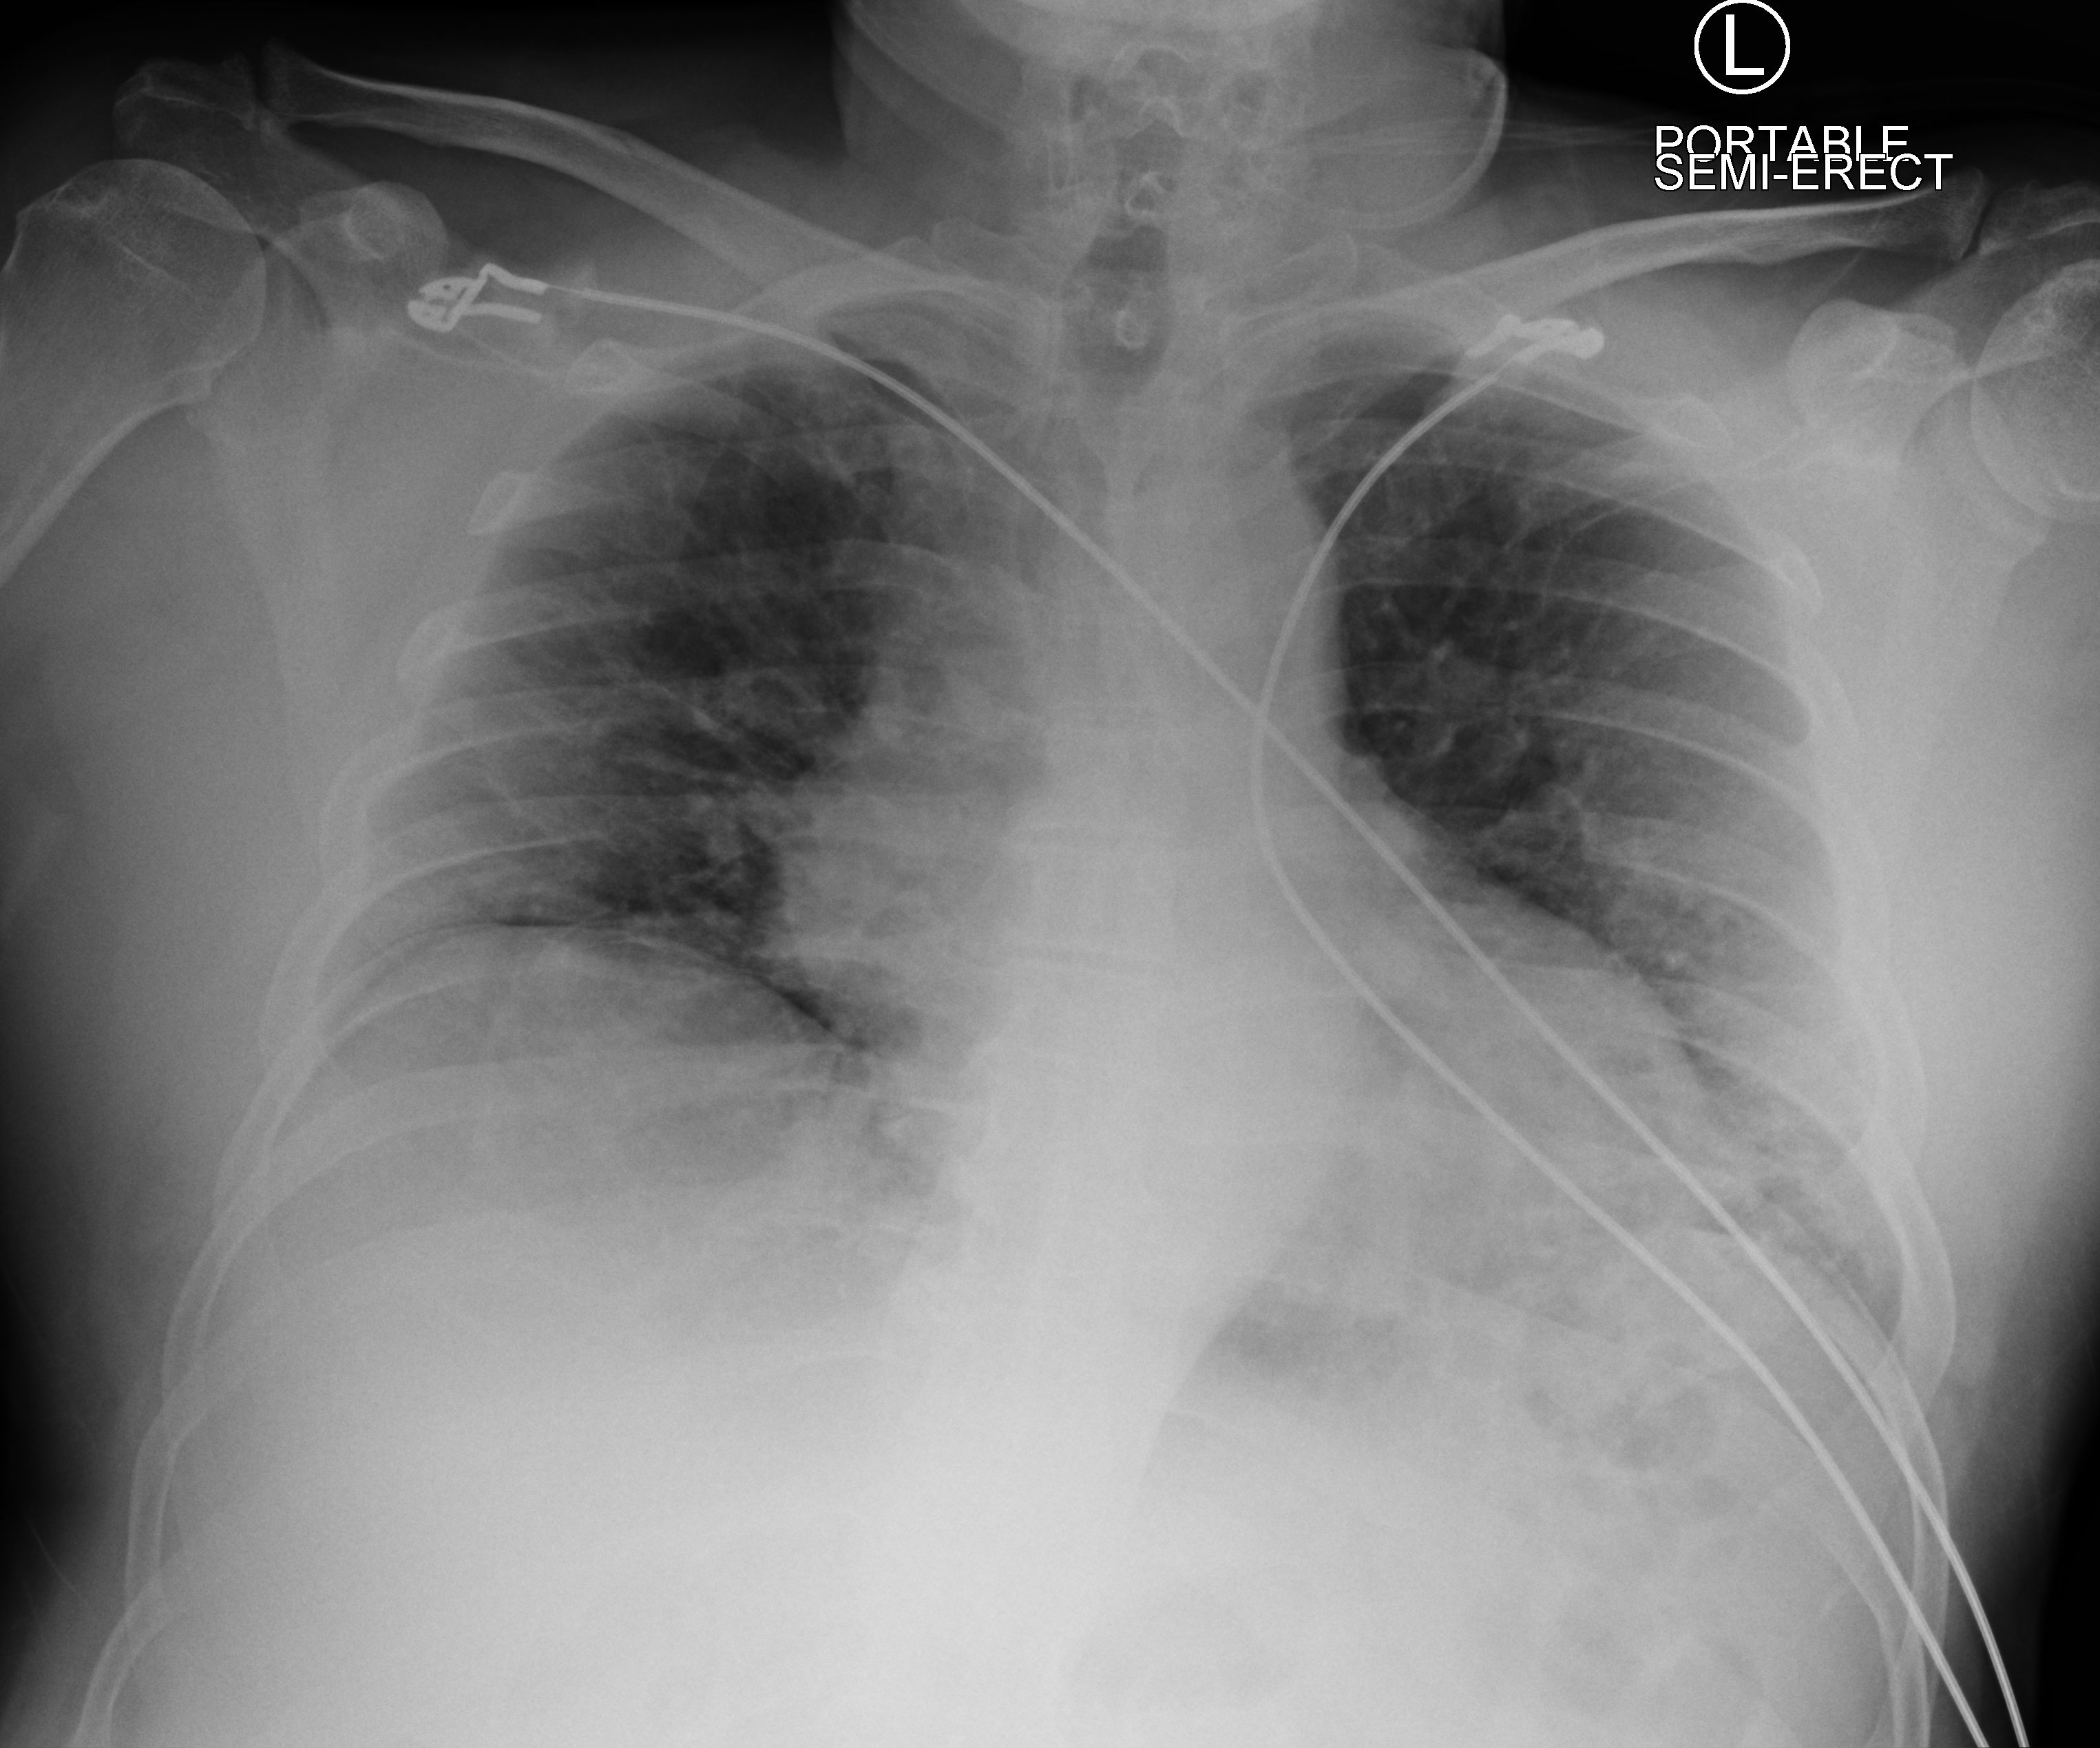
Chest X-ray (portable), anteroposterior (AP) projection. Patient hospitalised with COVID-19; male, aged 18–59 years.
From the hospital-stay record, not from the radiograph (when in the stay this image was taken is not recorded): diabetes (admission record): no.